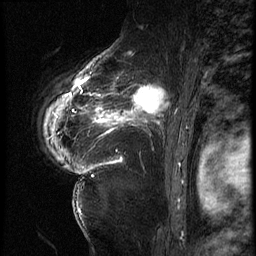
Breast MRI (dynamic contrast-enhanced), one sagittal slice. Position 47 of 62 along the scan axis. 3 images stored at this slice position (order not interpretable as contrast timing). 1.5 T. TE 4.2 ms, TR 9 ms. 2.5 mm slice thickness. 256 × 256 image matrix. Patient: female, 56 years. Case-level facts recorded for this patient, not image findings: setting: breast cancer imaged before/during neoadjuvant chemotherapy; receptor status: HER2-positive.
Structures marked on this image (semi-automatically segmented with operator editing):
- analysis volume of interest (the breast-tissue region the enhancement analysis was run in; not a lesion): bounding box <84,75,181,153> (left, top, right, bottom; pixels)
- tumour enhancement mask (voxels above the 140 % enhancement threshold inside the analysis volume of interest): <84,75,171,135>